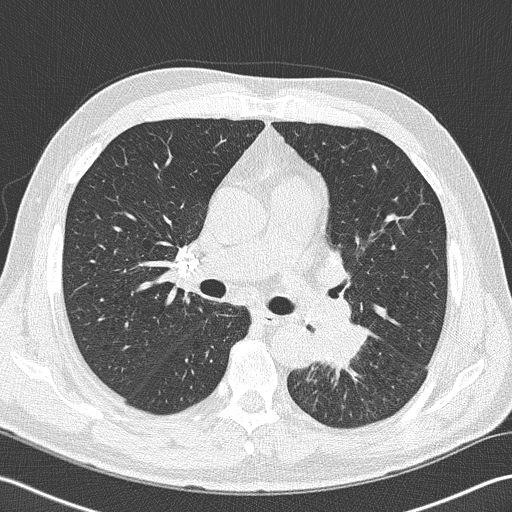
Axial slice from a low-dose chest CT screening exam. Second screening round (one year after baseline). Lung window (W 1500 / L -600 HU). 120 kVp. 512 × 512 image matrix, field of view 350 × 350 mm. Male, age 57 years at enrolment. Former smoker at enrolment.
Expert-annotated lung lesion, bounding box (x1, y1, x2, y2) in pixels: (294, 308, 374, 384). Reader record for this screening exam (exam-level; its link to the box is not recorded): non-calcified nodule or mass ≥4 mm, left lower lobe, 40 × 30 mm, spiculated (stellate) margins, soft tissue attenuation, pre-existing on the prior screen: no. Official screen result: positive, other. Lung cancer was diagnosed 9 days after this screen: squamous cell carcinoma, NOS, left lower lobe, moderately differentiated (G2), stage IIIB (AJCC 6th edition), 38 mm at pathology.